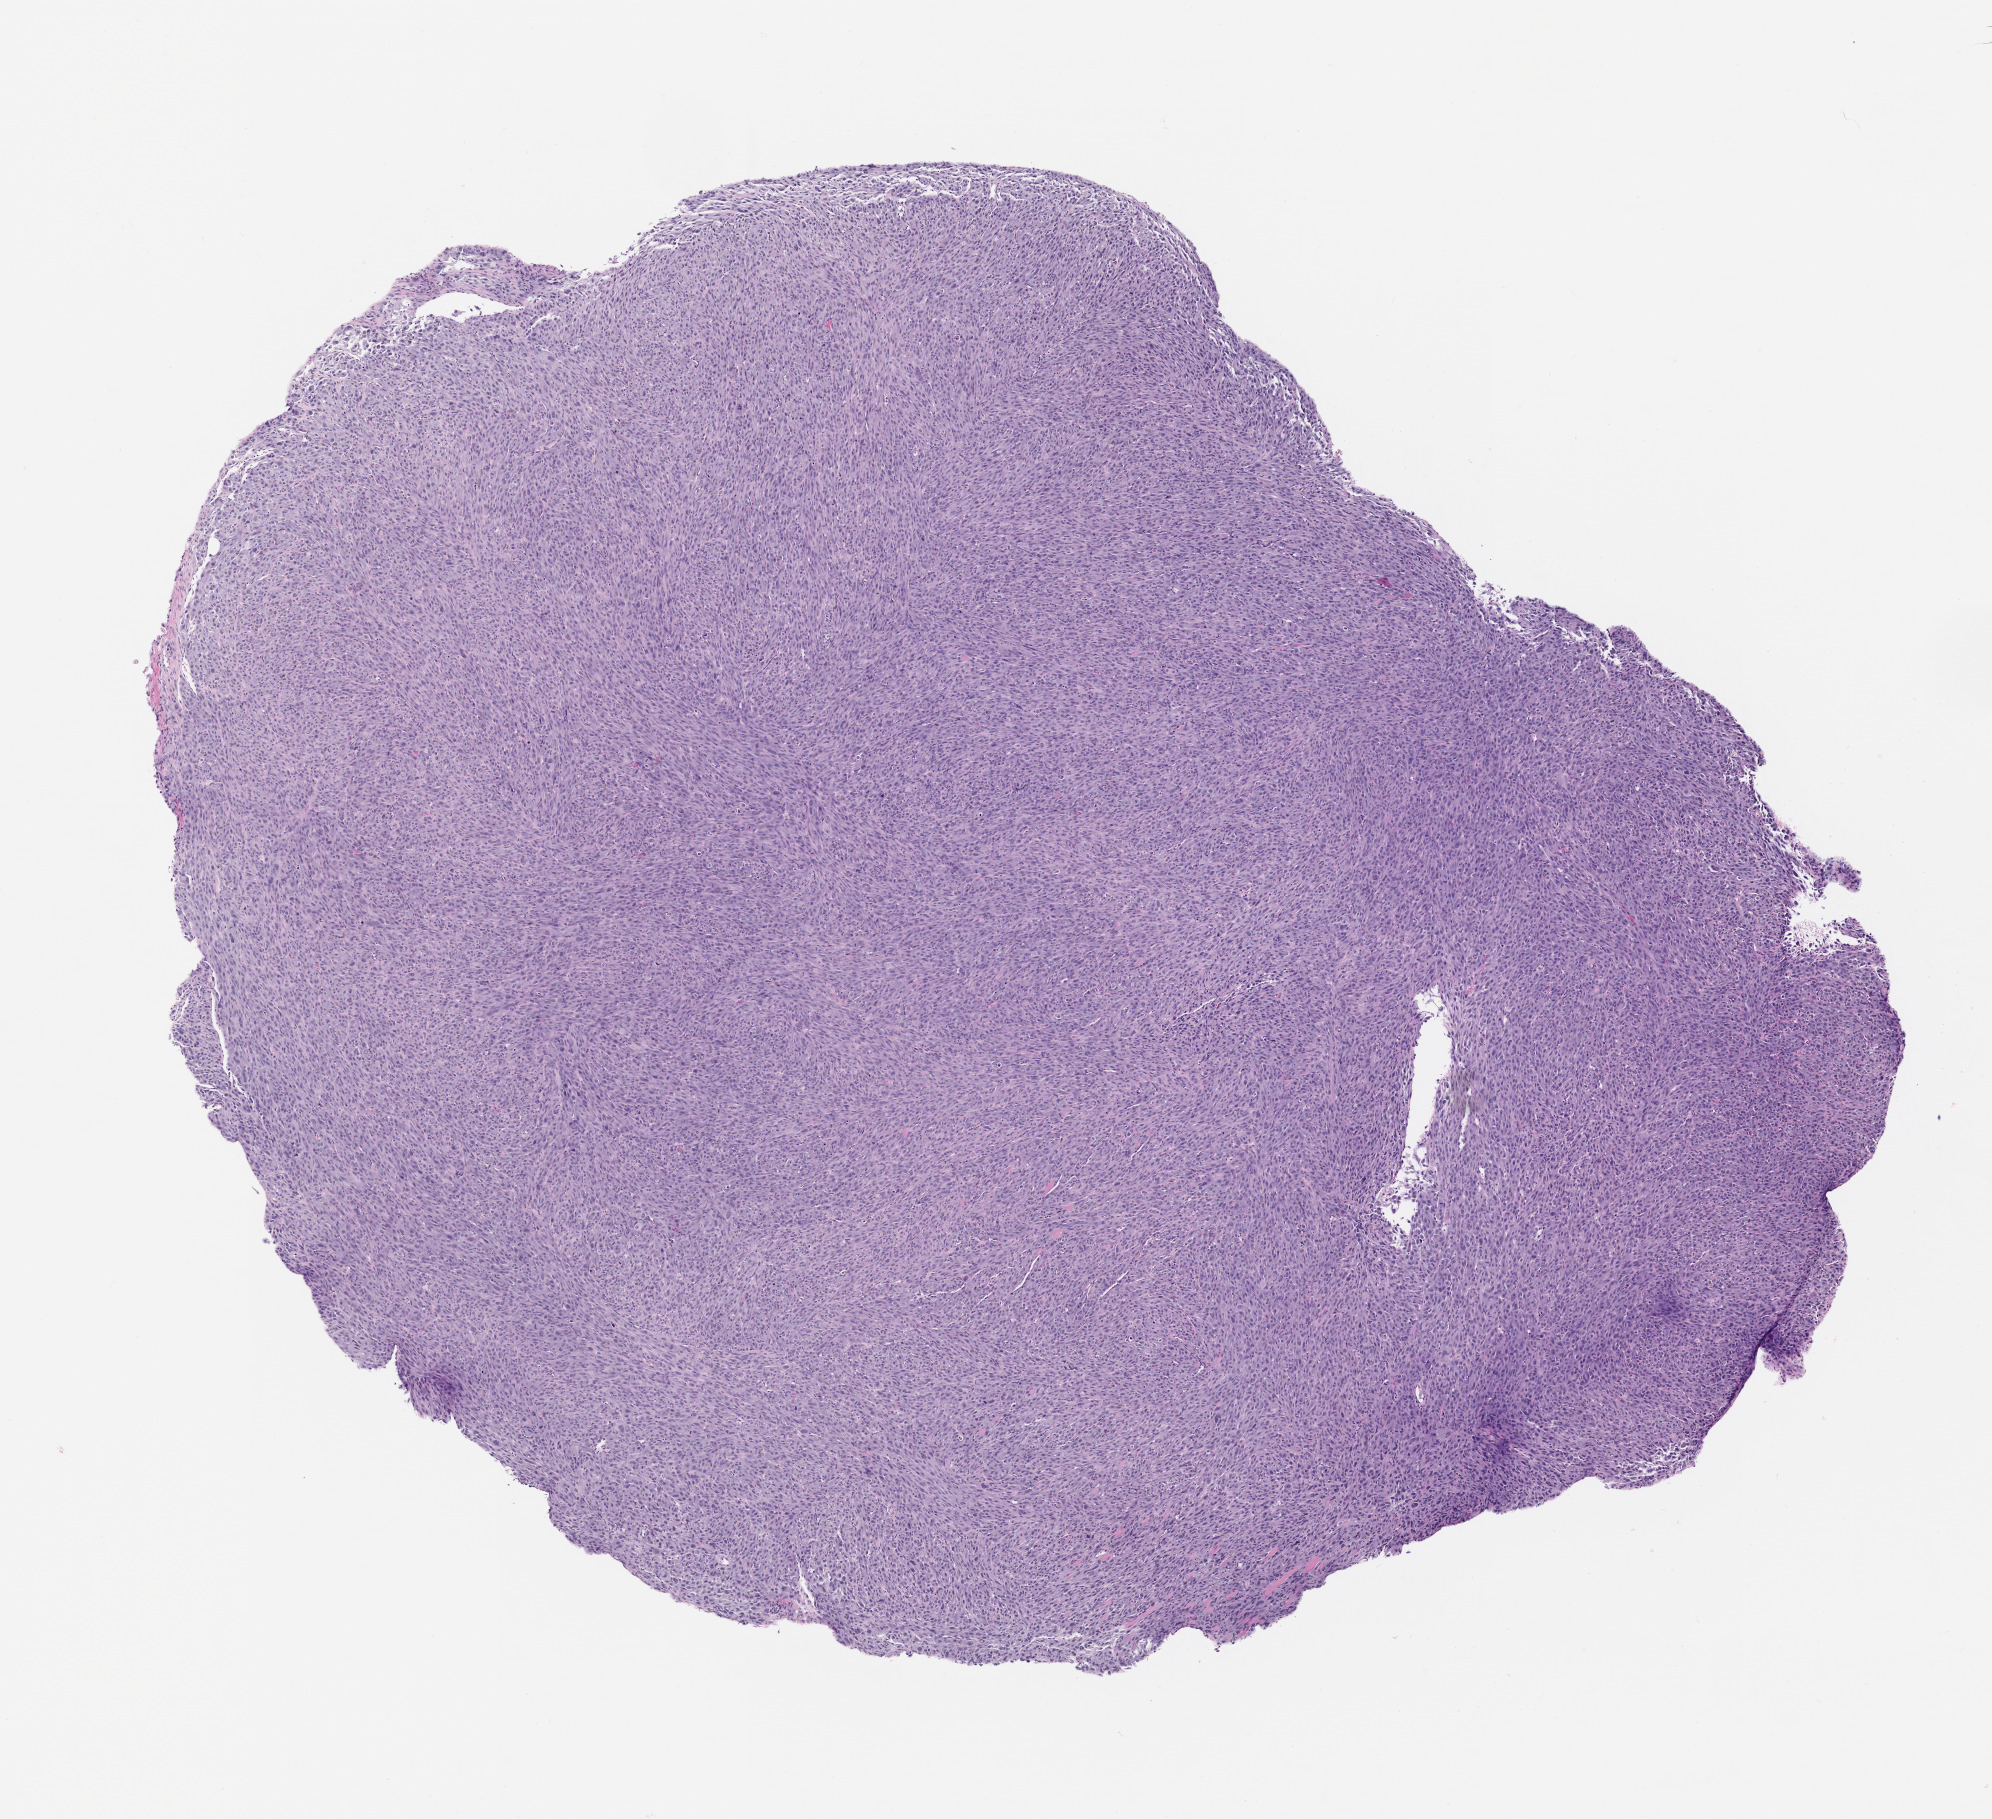
Hematoxylin and eosin (H&E) whole-slide image of a patient-derived xenograft (PDX) tumor grown in a mouse, passage 1, whole scanned area (about 8.0 x 7.3 mm) shown as a low-resolution overview. FFPE section. Originating tumor site category: bone.
Originating patient diagnosis: Osteosarcoma.